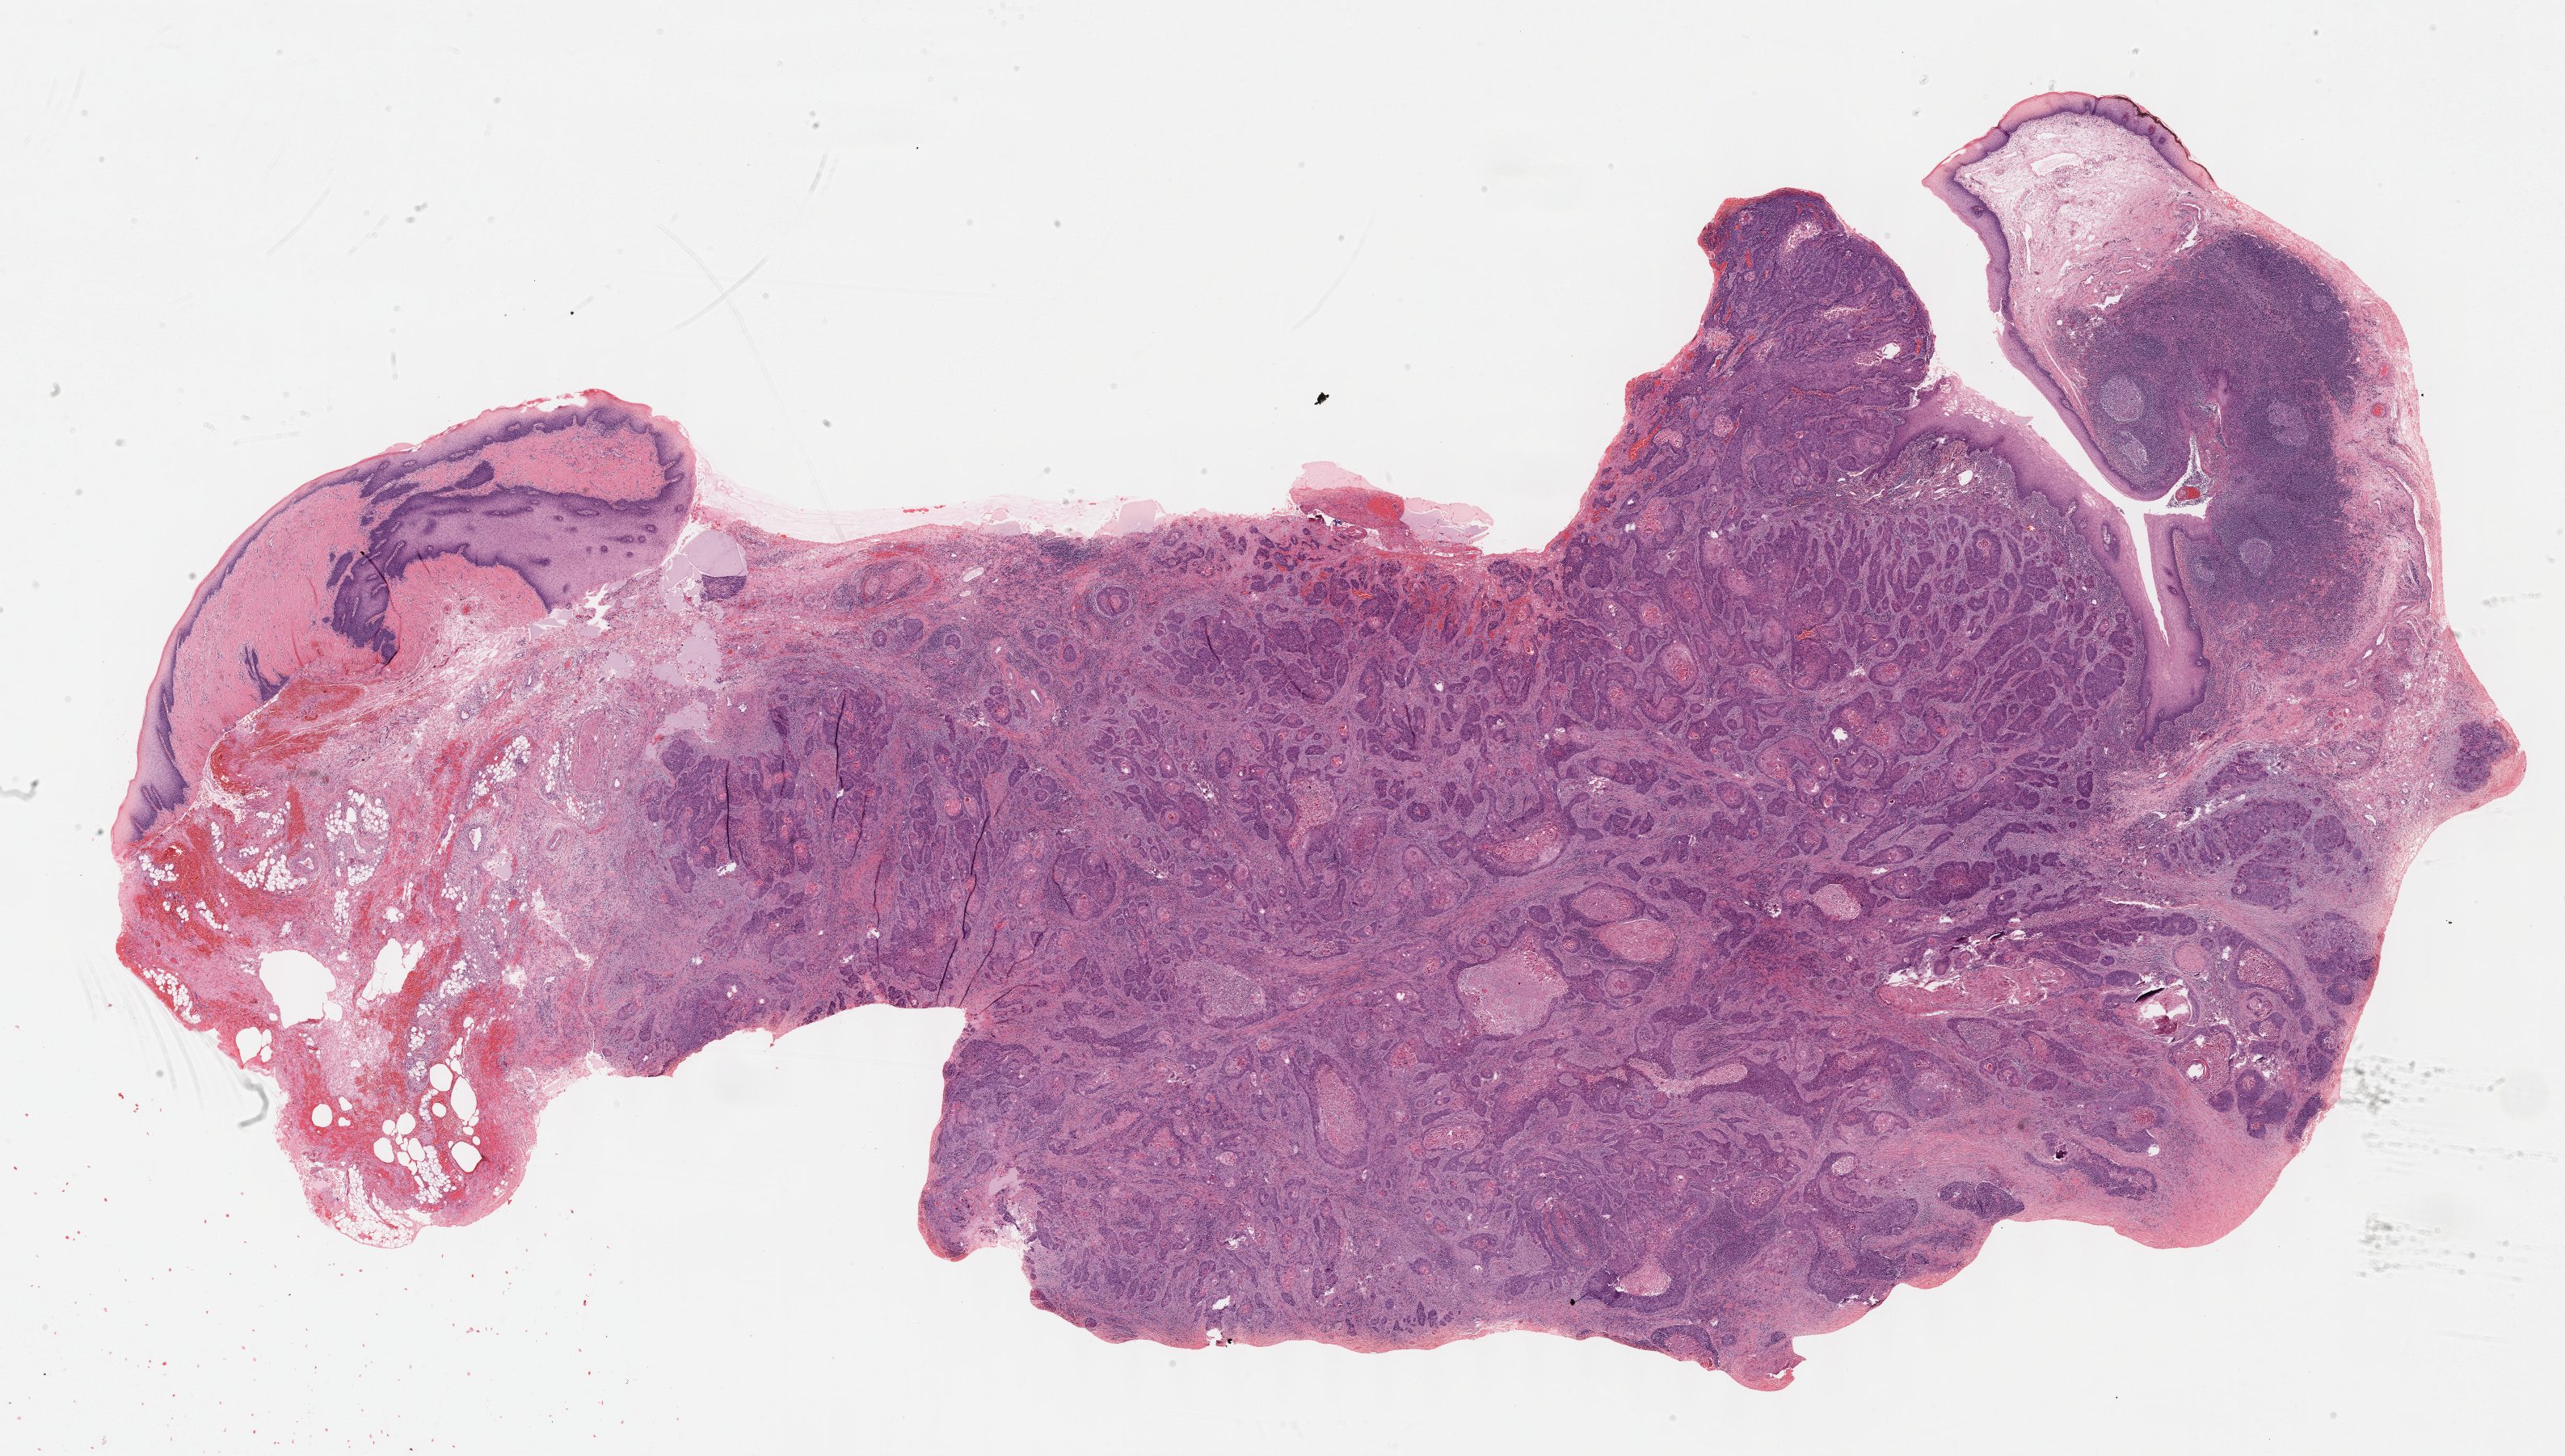
Whole-slide histology image, H&E — shown as a low-resolution overview of the whole scanned area (about 25.7 x 14.6 mm, slide scanned at 40x), formalin-fixed paraffin-embedded (FFPE) diagnostic section, sample: primary tumour, head and neck. Patient: female, age at initial diagnosis 63 years. Histologic grade: G2 (moderately differentiated).
AJCC pathologic stage: IVA (7th edition). Histologic diagnosis: Squamous cell carcinoma, NOS (larynx, NOS).